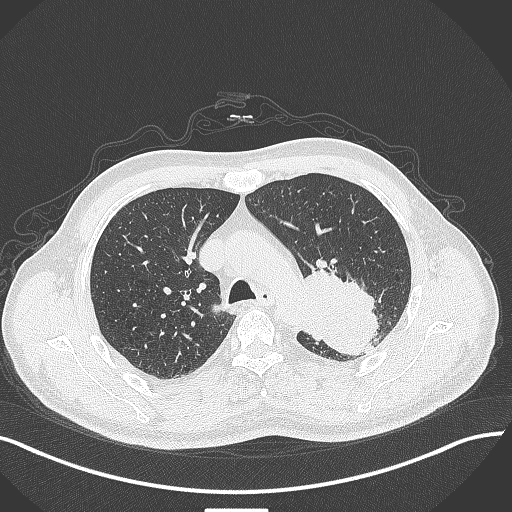
Chest CT, one axial slice. Position 303 of 429 along the scan axis. Reconstruction kernel B70f. Lung window (W 1500 / L -600 HU). 1 mm slice thickness. 512 × 512 image matrix, field of view 400 × 400 mm. Male patient, age 55 years. Case-level facts recorded for this patient, not image findings: clinical TNM (as recorded): T3 N0 M1c.
Outlined on this slice (rectangle marked by the reading radiologist):
- lung tumour (recorded histology: adenocarcinoma): bounding box <300,264,380,356> (left, top, right, bottom; pixels)